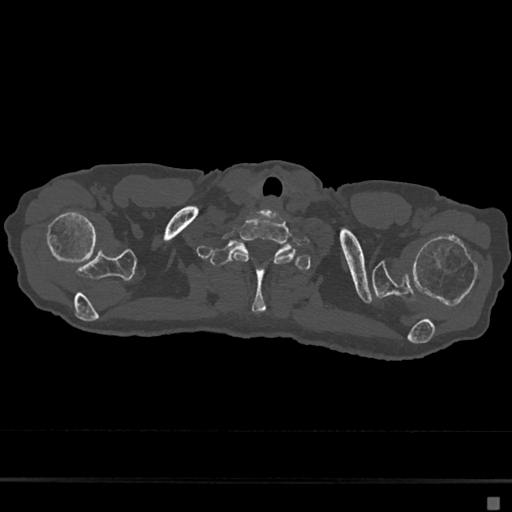
CT including the spine, one axial slice; slice 627 of 797 in the series (ordered by position); reconstruction kernel Br40s/3; bone window (W 1800 / L 400 HU); 0.5 mm slice thickness; 512 × 512 image matrix, field of view 360 × 360 mm. Patient: female, 68 years. From the clinical record (not read from this slice): primary cancer: renal.
Outlined on this slice (semi-automatically segmented with operator editing):
- T1 vertebra: bounding box (x1, y1, x2, y2) in pixels: (209, 242, 311, 313)